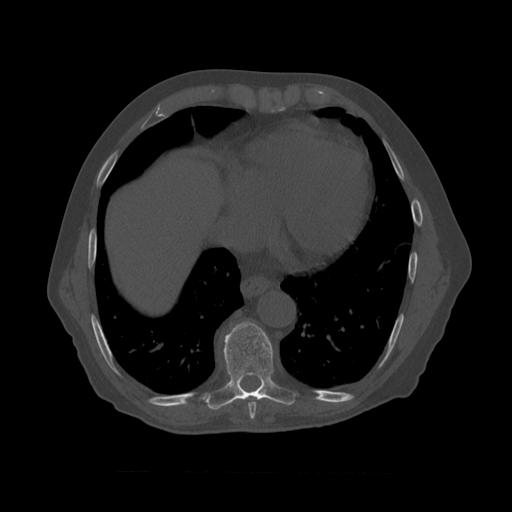
CT including the spine, one axial slice. Slice 449 of 450 in the series (ordered by position). Reconstruction kernel STANDARD. Bone window (W 1800 / L 400 HU). 1.25 mm slice thickness. 512 × 512 image matrix, field of view 405 × 405 mm. Patient age 75 years. Case-level facts recorded for this patient, not image findings: primary cancer: prostate.
Annotated regions visible in this slice (semi-automatic segmentation, software-assisted and operator-edited):
- T8 vertebra: bounding box [x1, y1, x2, y2] px = [219, 322, 296, 411]